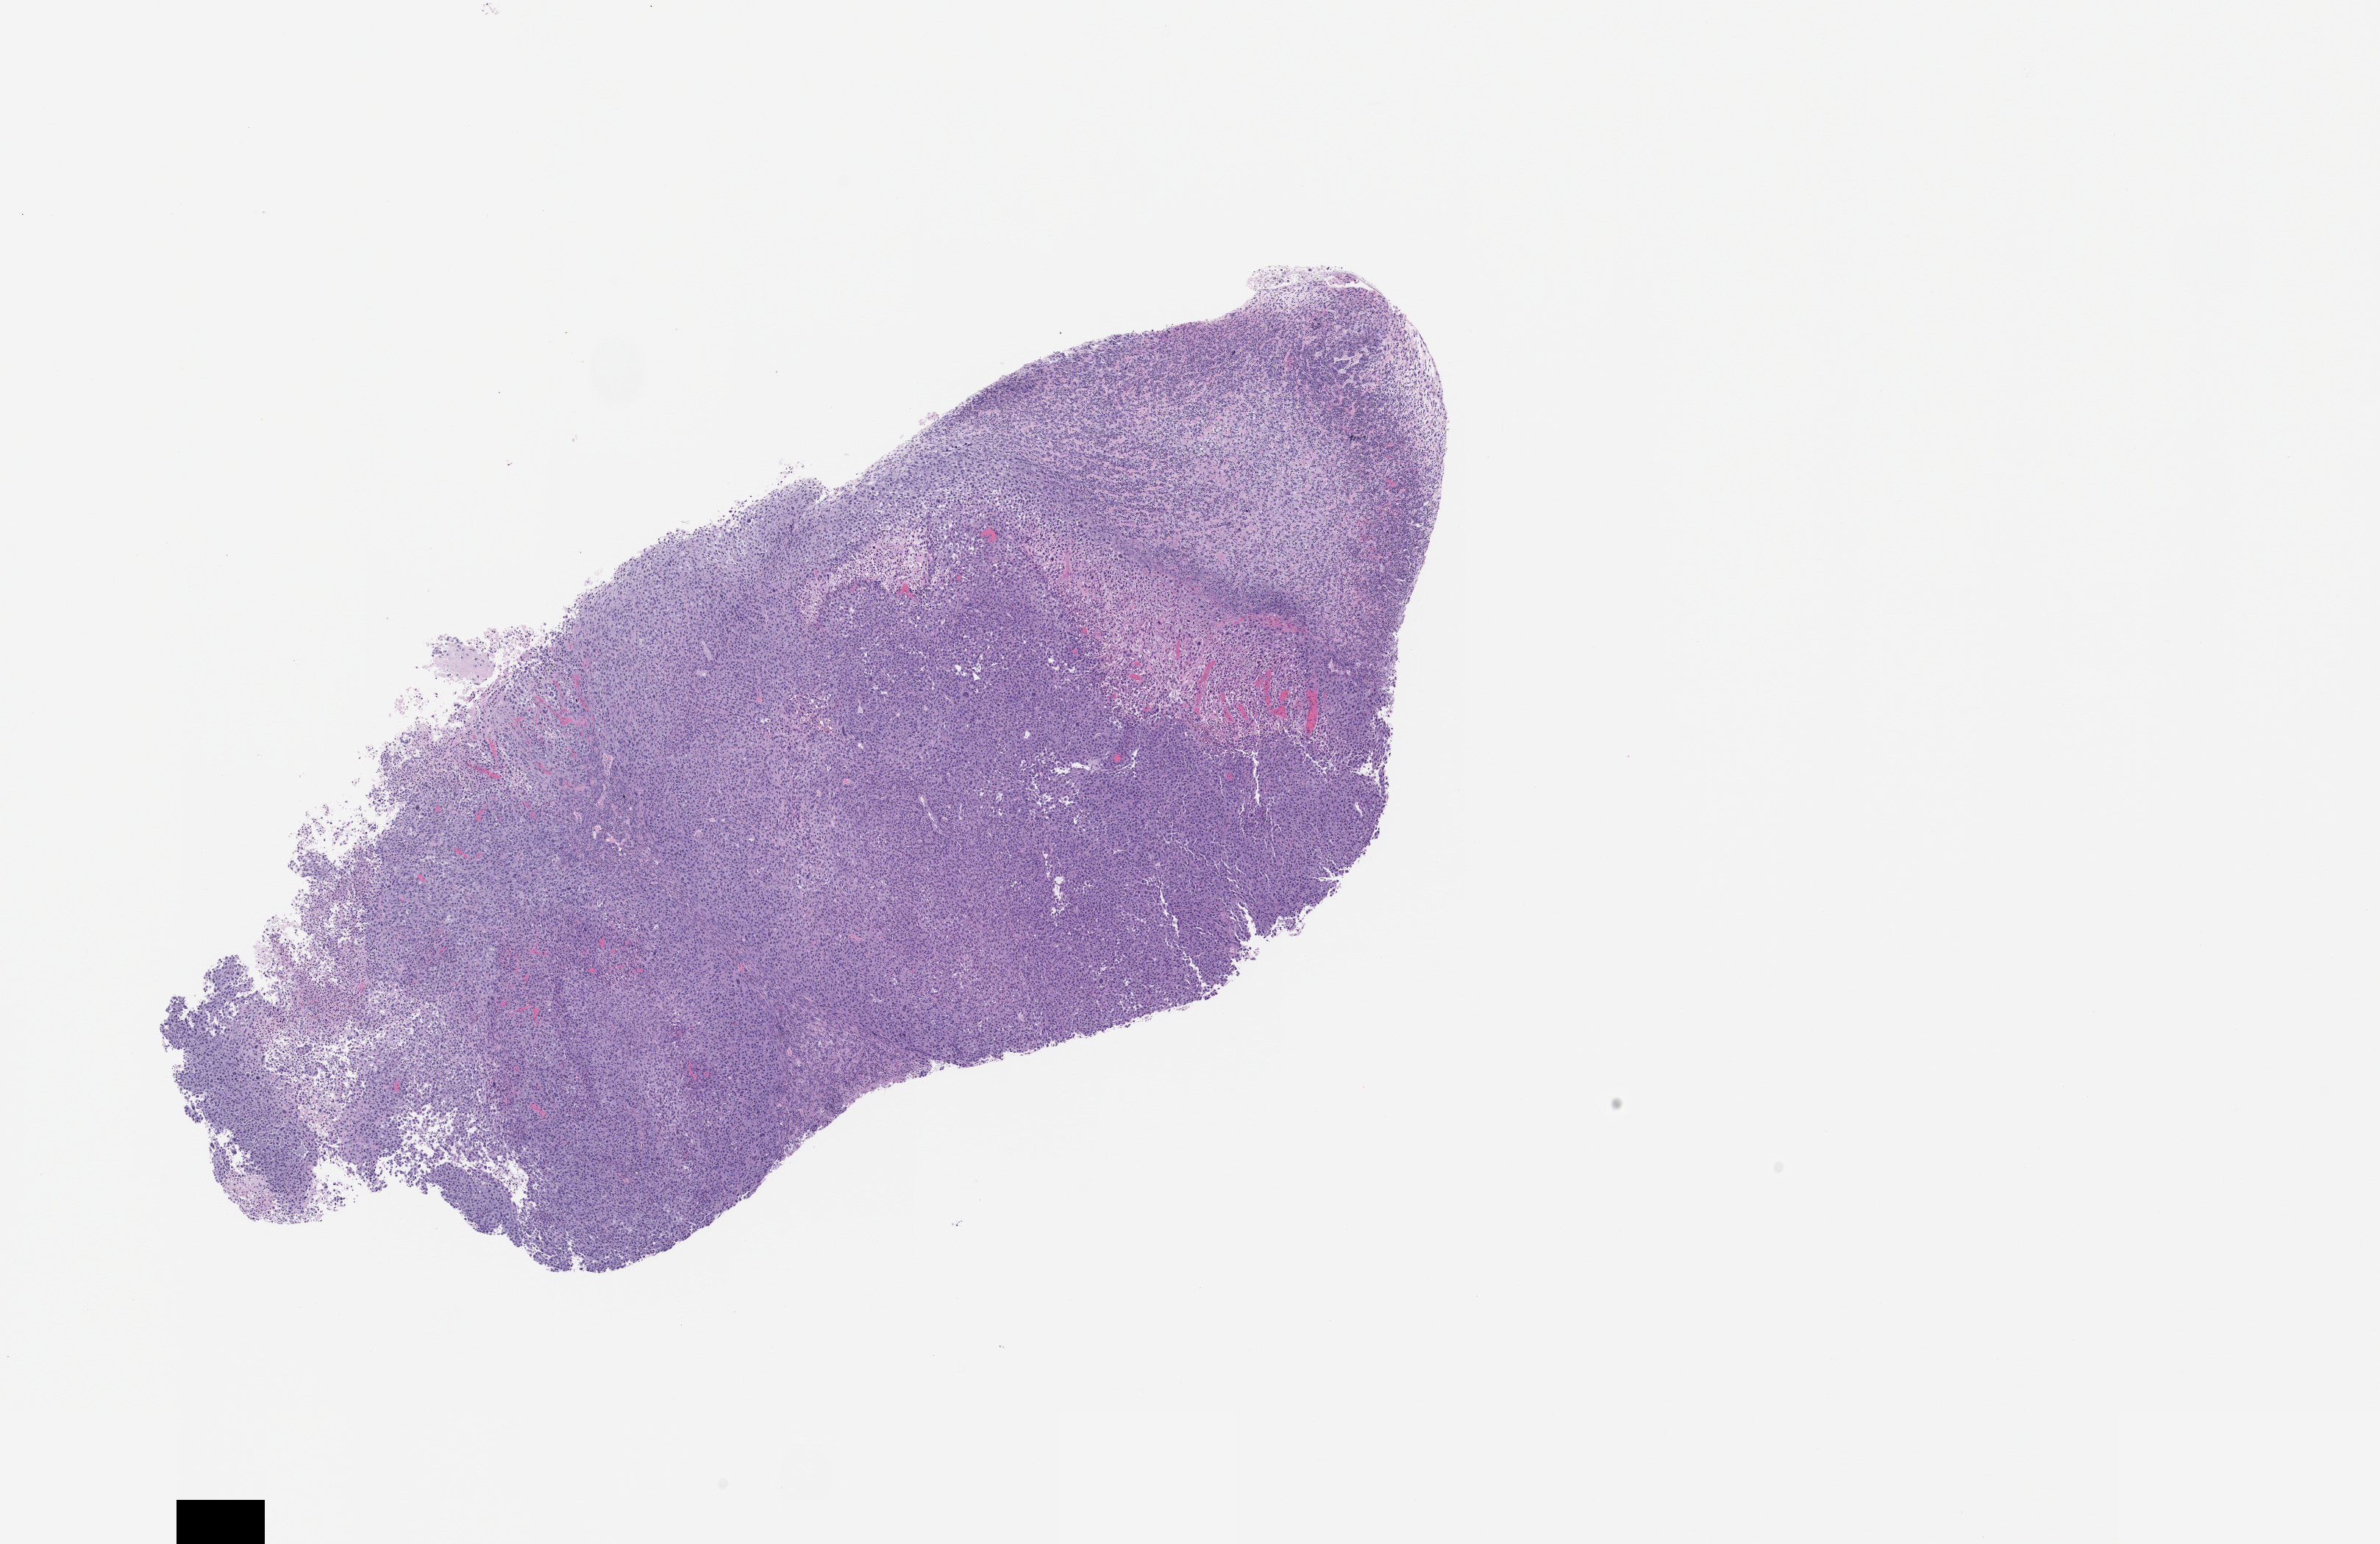
Hematoxylin and eosin (H&E) whole-slide image of a patient-derived xenograft (PDX) tumor grown in a mouse, passage 2, whole scanned area (about 13.0 x 8.4 mm) shown as a low-resolution overview. Formalin-fixed paraffin-embedded section. Originating tumor site category: head and neck.
- originating patient diagnosis: Head and Neck Squamous Cell Carcinoma